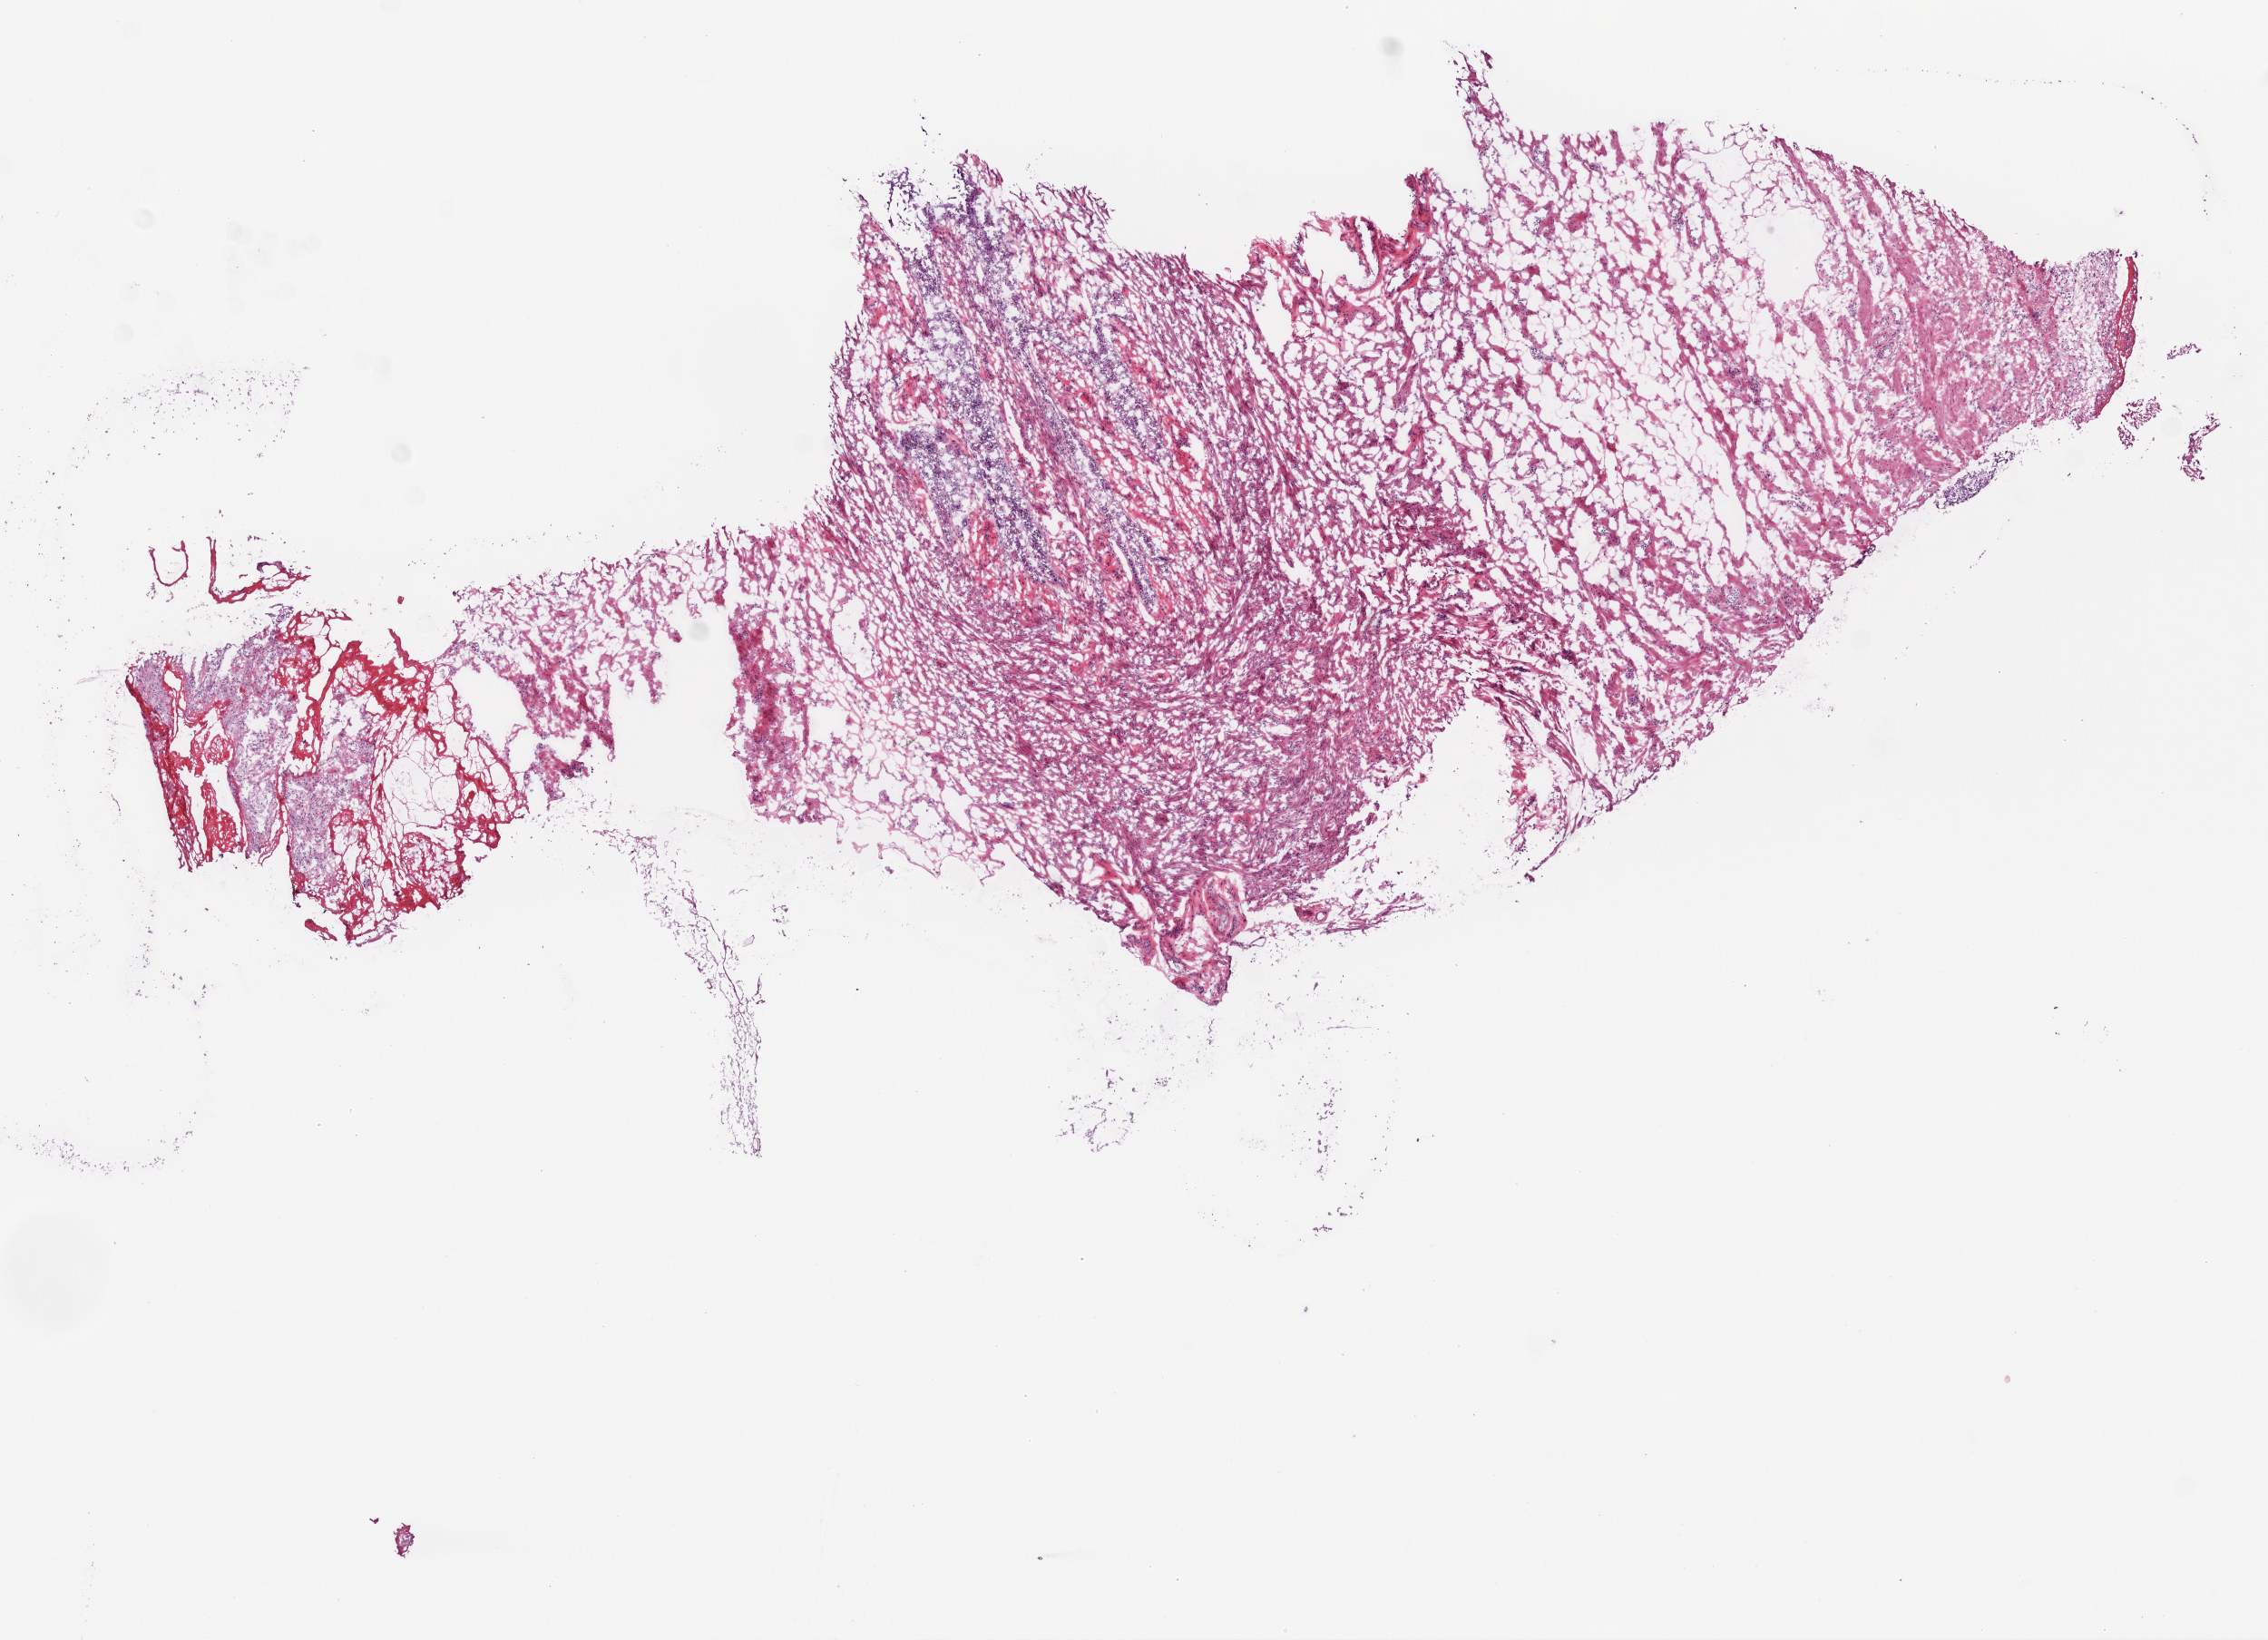
Whole-slide histology image, H&E-stained — low-resolution overview of the scanned area, about 10.0 x 7.3 mm (acquisition: 20x scan). Frozen section. Solid tissue normal (non-tumour tissue) sample from the ovary. Patient: female, age at initial diagnosis 53 years.
This section: solid tissue normal sample (biorepository sample class). Patient diagnosis: Serous surface papillary carcinoma.